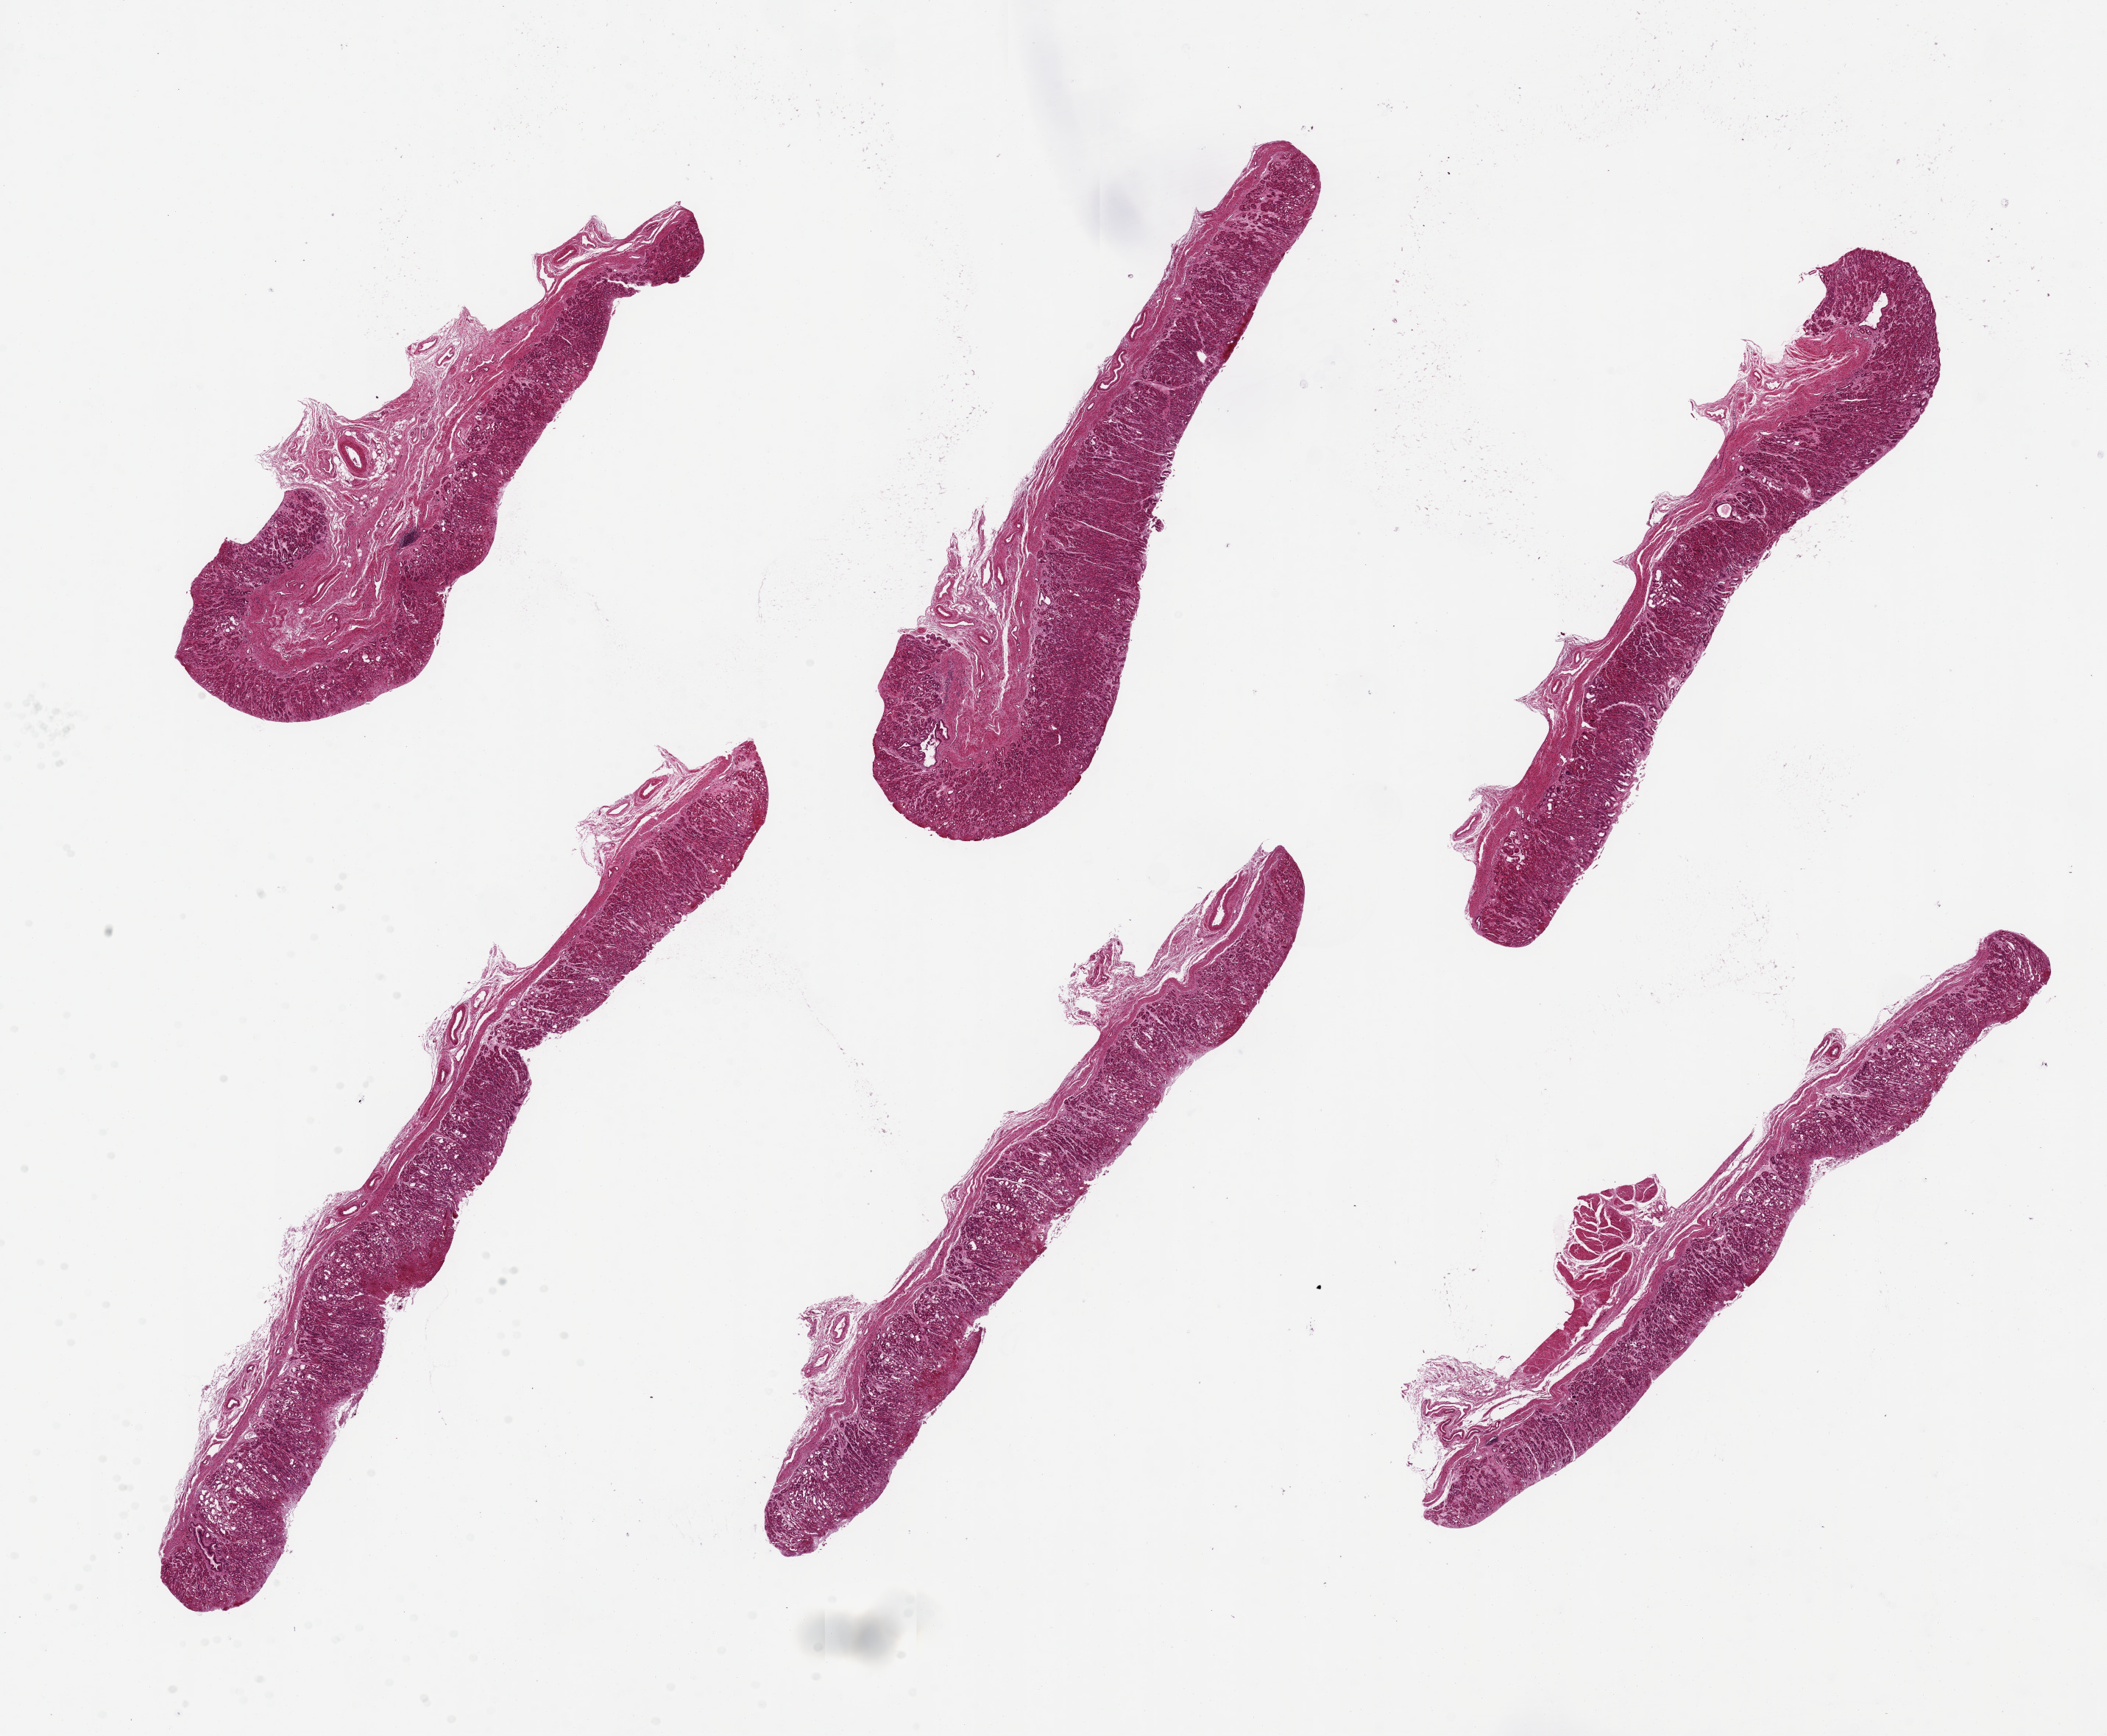
Hematoxylin and eosin (H&E) whole-slide image, low-resolution overview of the scanned area, about 22.6 x 18.7 mm (from a 20x scan); PAXgene-fixed, paraffin-embedded tissue; sampled site (target tissue): stomach; tissue donor sample. Donor sex: male.
Reviewer comment on this tissue sample: 6 pieces, up to 11x1.4 mm; all mucosa & submucosa.